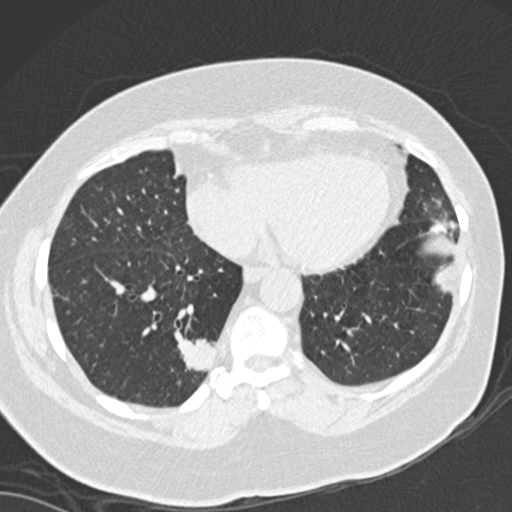
Low-dose screening chest CT, one axial slice; slice 53 of 162 in the series (ordered by position); reconstruction kernel B30f; lung window (W 1500 / L -600 HU); 2 mm slice thickness; 512 × 512 image matrix.
Outlined on this slice (manually delineated by an expert):
- lesion 1 (tumor, lower lobe of right lung): bounding box (x1, y1, x2, y2) in pixels: (178, 339, 215, 372)